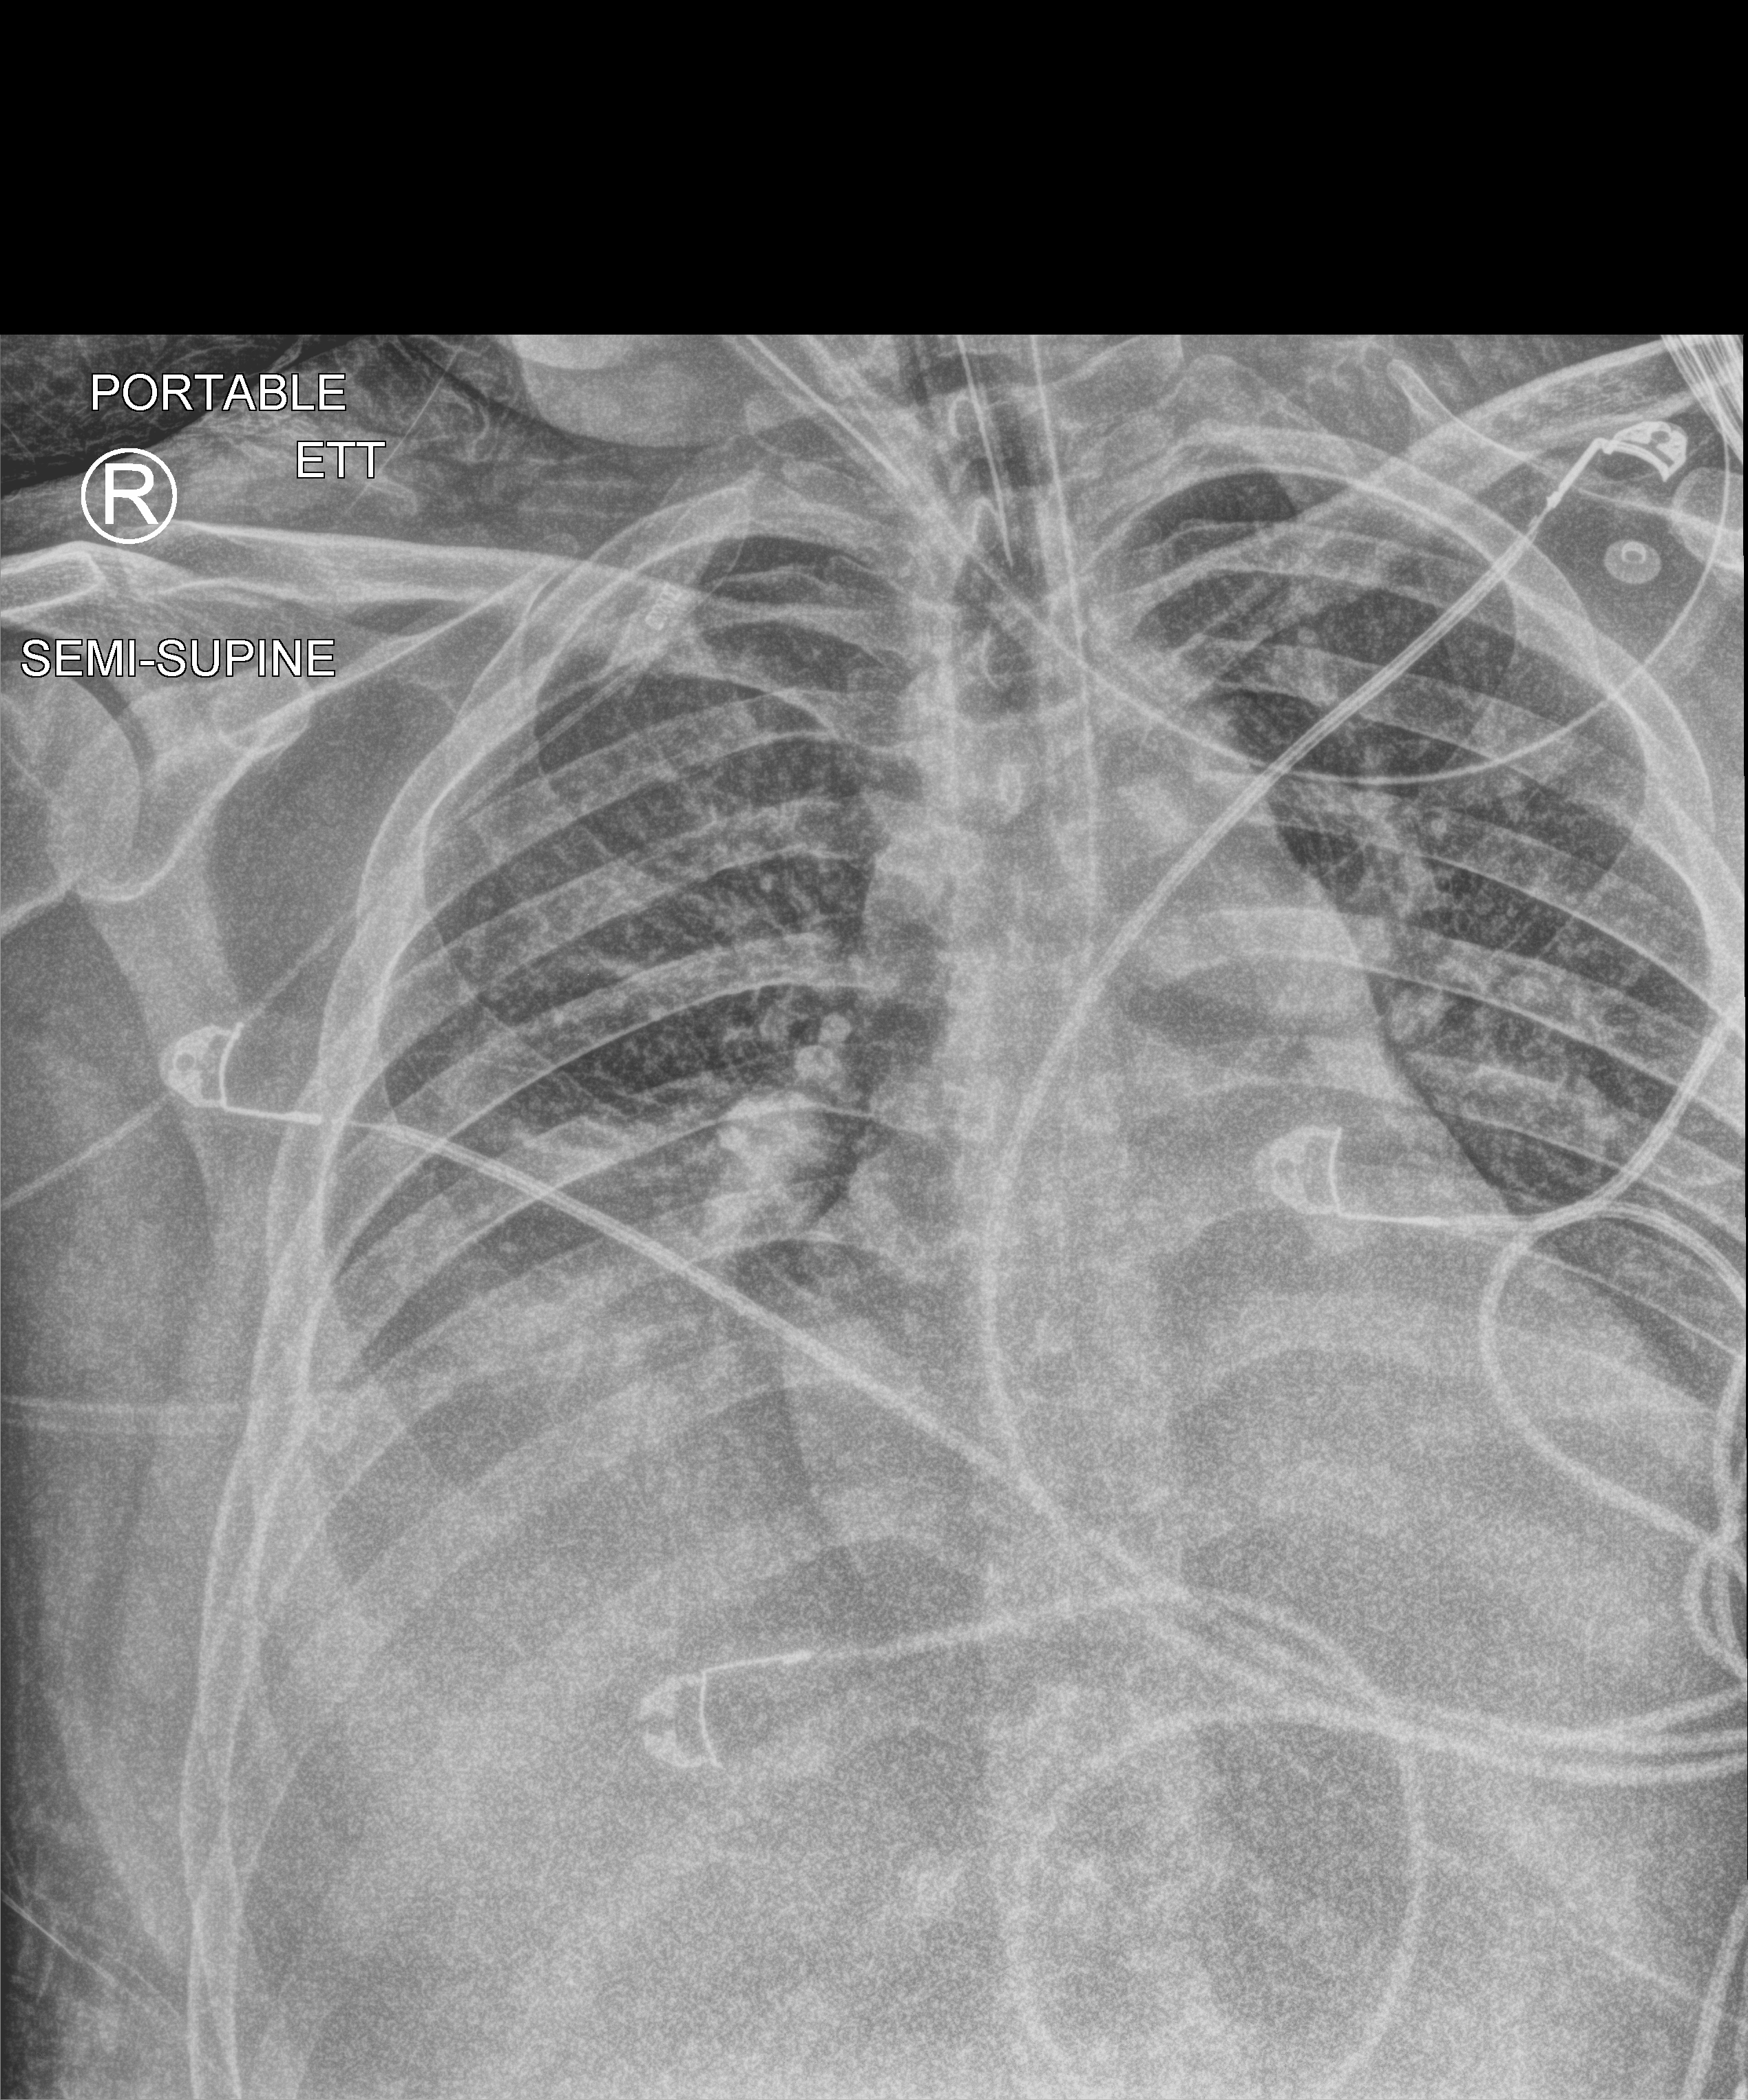
Portable chest radiograph; anteroposterior (AP) projection. Patient hospitalised with COVID-19; male, aged 18–59 years.
Hospital-stay facts (about this admission, not read from this image; timing relative to this image not recorded):
- mechanically ventilated during this hospital stay: yes
- diabetes (admission record): no